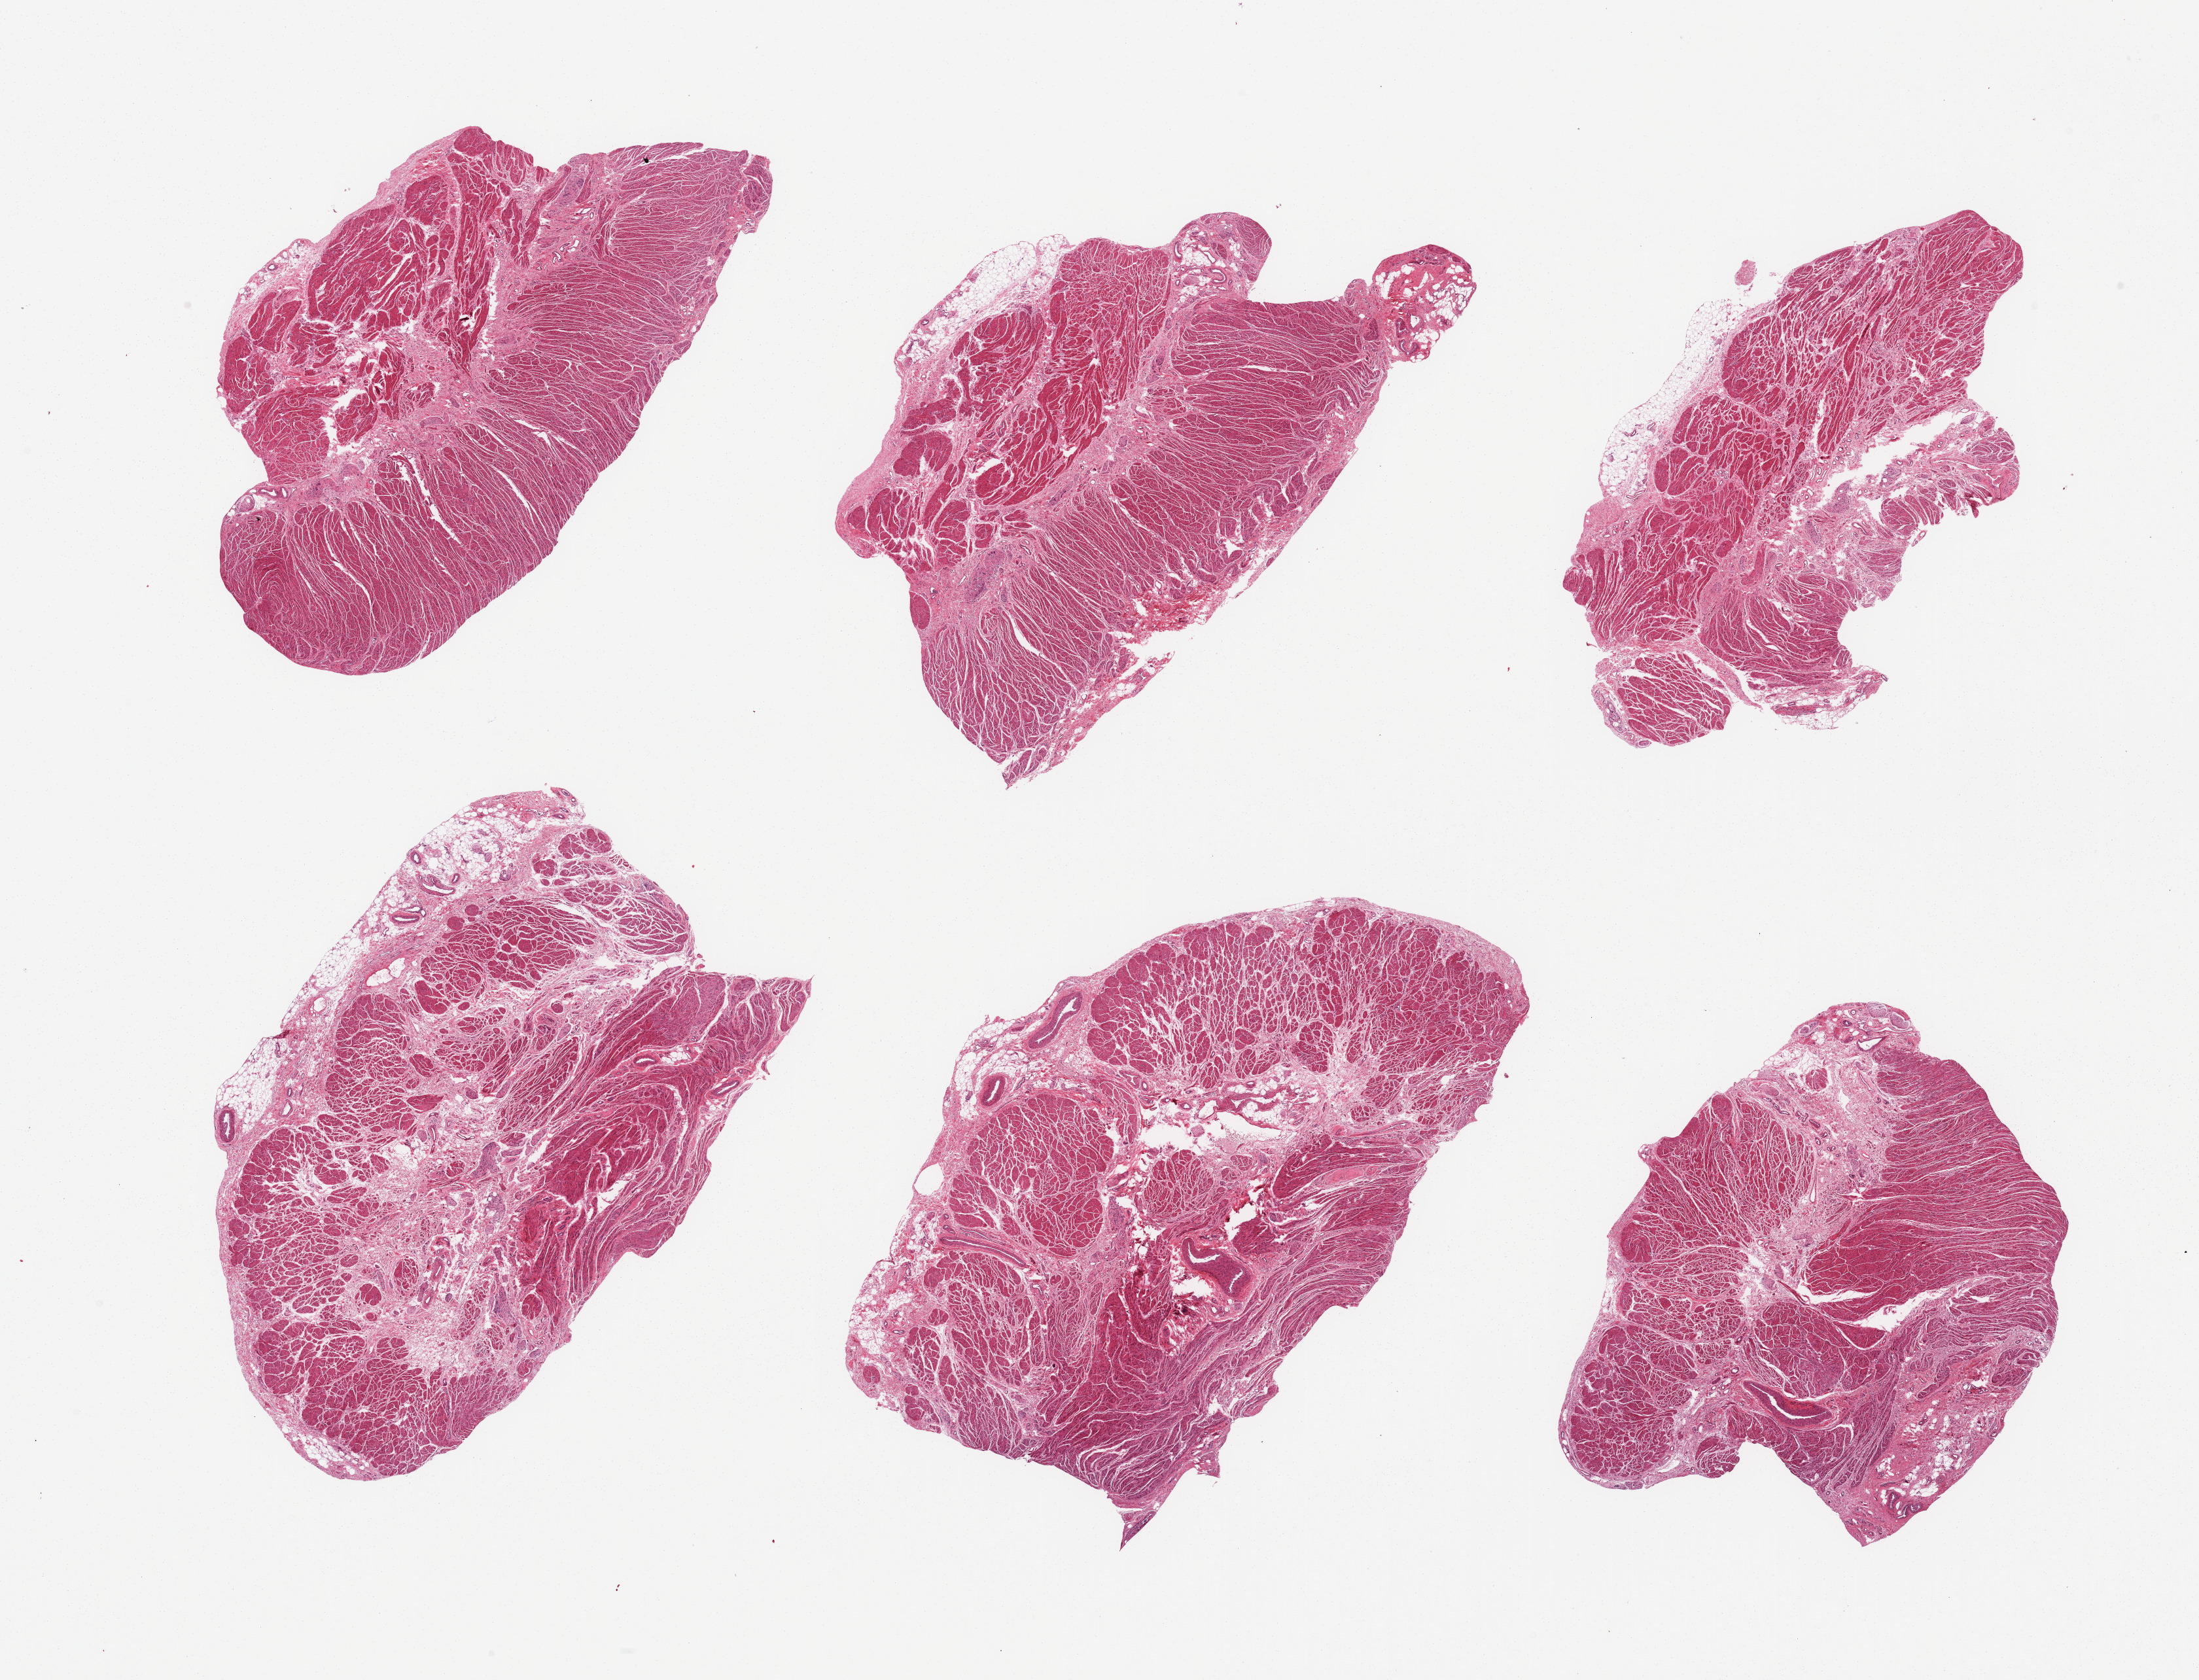
H&E whole-slide image, low-resolution overview of the scanned area, about 26.6 x 20.3 mm, PAXgene-fixed paraffin-embedded (PFPE) section, section of gastroesophageal junction (target tissue), tissue donor sample. Male donor.
Review note (as recorded): 6 pieces; well dissected.